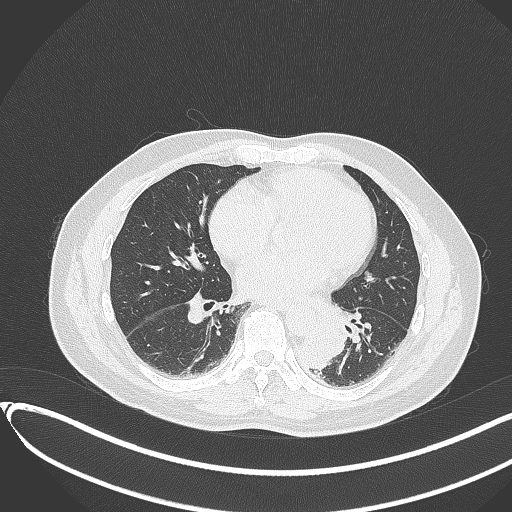
Chest CT, one axial slice. Position 143 of 417 along the scan axis. Reconstruction kernel B70f. 120 kVp. Lung window (W 1500 / L -600 HU). 1 mm slice thickness. 512 × 512 image matrix, field of view 400 × 400 mm. Patient: male, 54 years. Case-level facts recorded for this patient, not image findings: clinical TNM (as recorded): T3 N0 M0.
Annotated regions visible in this slice (rectangle marked by the reading radiologist):
- lung tumour (recorded histology: squamous cell carcinoma): bounding box (x1, y1, x2, y2) in pixels: (297, 318, 346, 372)